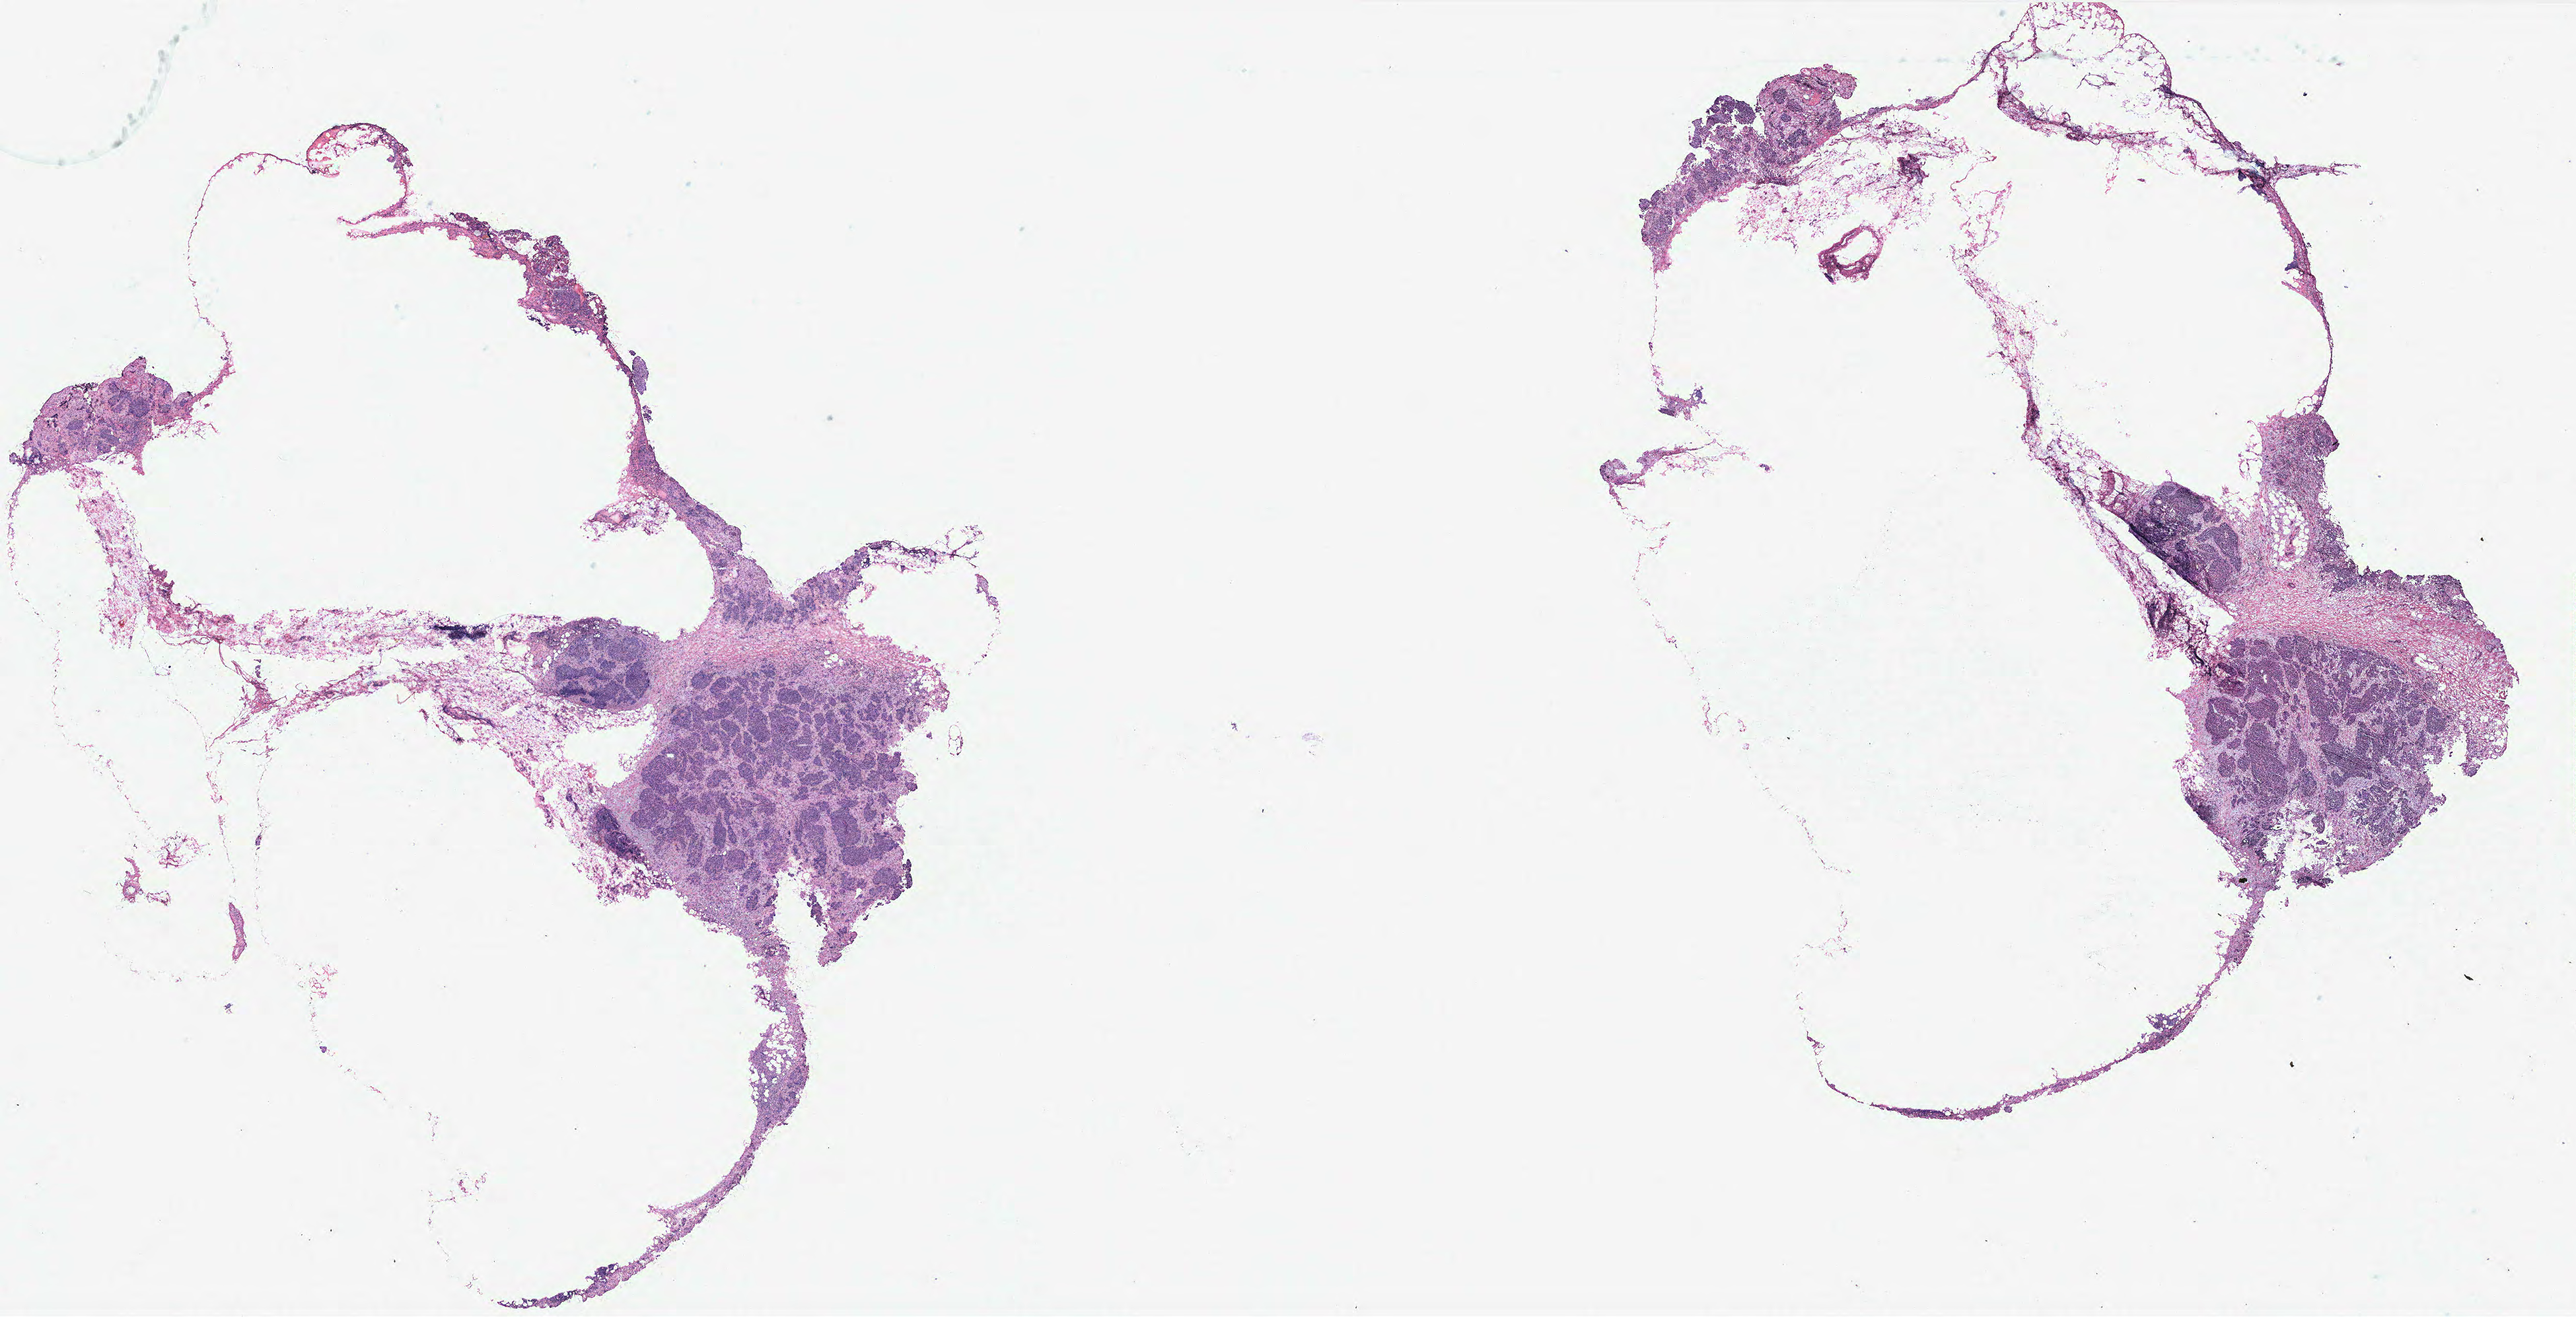
Digitized H&E-stained tissue section (whole slide), low-resolution overview of the scanned area, about 31.2 x 16.0 mm (slide scanned at 40x); ovary, tumour tissue. Patient: female, age 63 years.
Histologic diagnosis: Serous adenocarcinoma, NOS (fallopian tube). Primary tumour site (as recorded): fallopian tube.